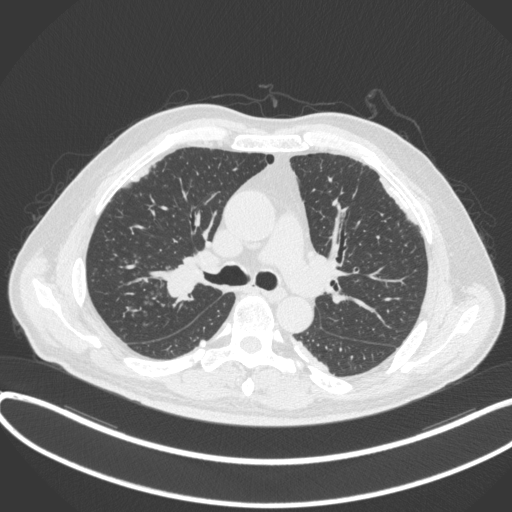
Chest CT, one axial slice; position 268 of 455 along the scan axis; reconstruction kernel B31f; 120 kVp; lung window (W 1500 / L -600 HU); 1 mm slice thickness; 512 × 512 image matrix. Male patient, age 58 years. Case-level facts recorded for this patient, not image findings: clinical TNM (as recorded): T1c N0 M0.
Structures marked on this image (rectangle marked by the reading radiologist):
- lung tumour (recorded histology: squamous cell carcinoma): box from (x=148, y=258) to (x=206, y=303) px